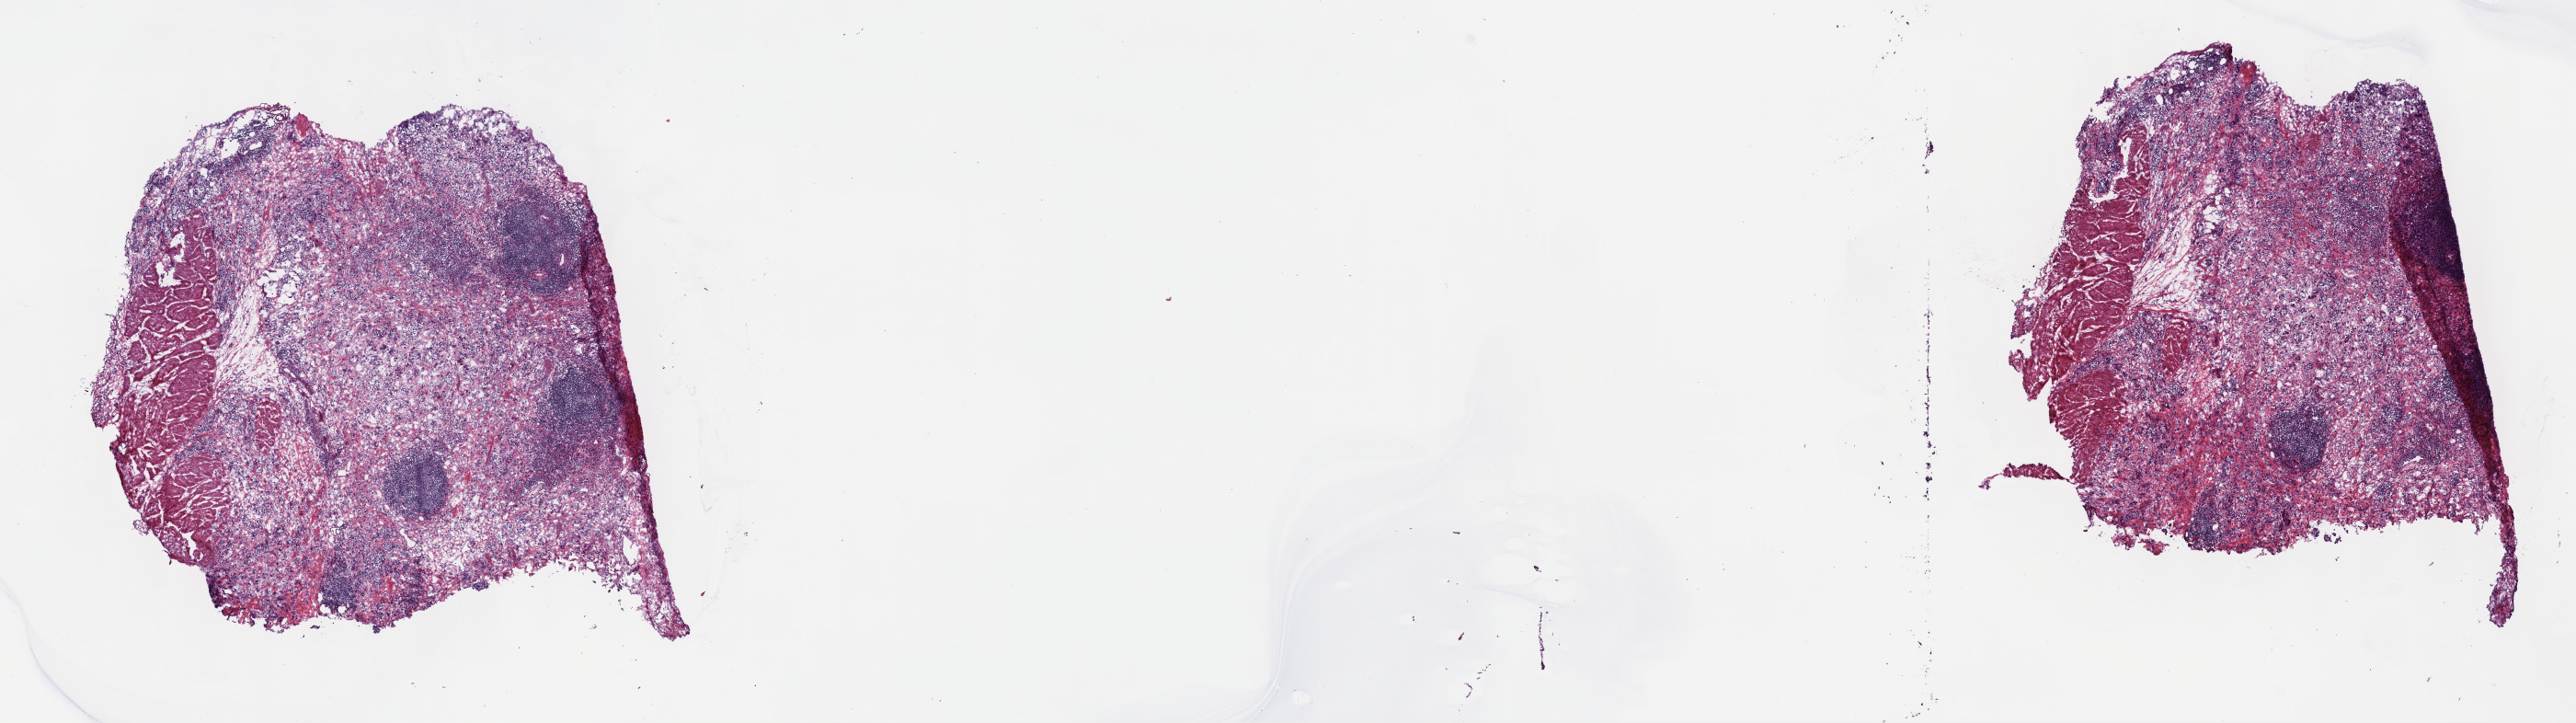
Whole-slide histology image, H&E-stained, low-resolution overview of the scanned area, about 22.7 x 6.4 mm (slide scanned at 40x); frozen section from the top of the tissue portion; bladder, primary tumour sample. Male patient; age at initial diagnosis 65 years. Histologic grade: high grade. Pathologist review of this section (percent, as recorded): tumour cells 60%, tumour nuclei 60%, normal cells 0%, stromal cells 39%, necrosis 1%. Inflammatory infiltration, as recorded: lymphocyte infiltration 12%, monocyte infiltration 1%, neutrophil infiltration 5%.
Histologic diagnosis: Transitional cell carcinoma (lateral wall of bladder). Lymph nodes positive (case pathology): 0 of 23 examined. AJCC pathologic stage: III. TNM: T3a N0 M0.